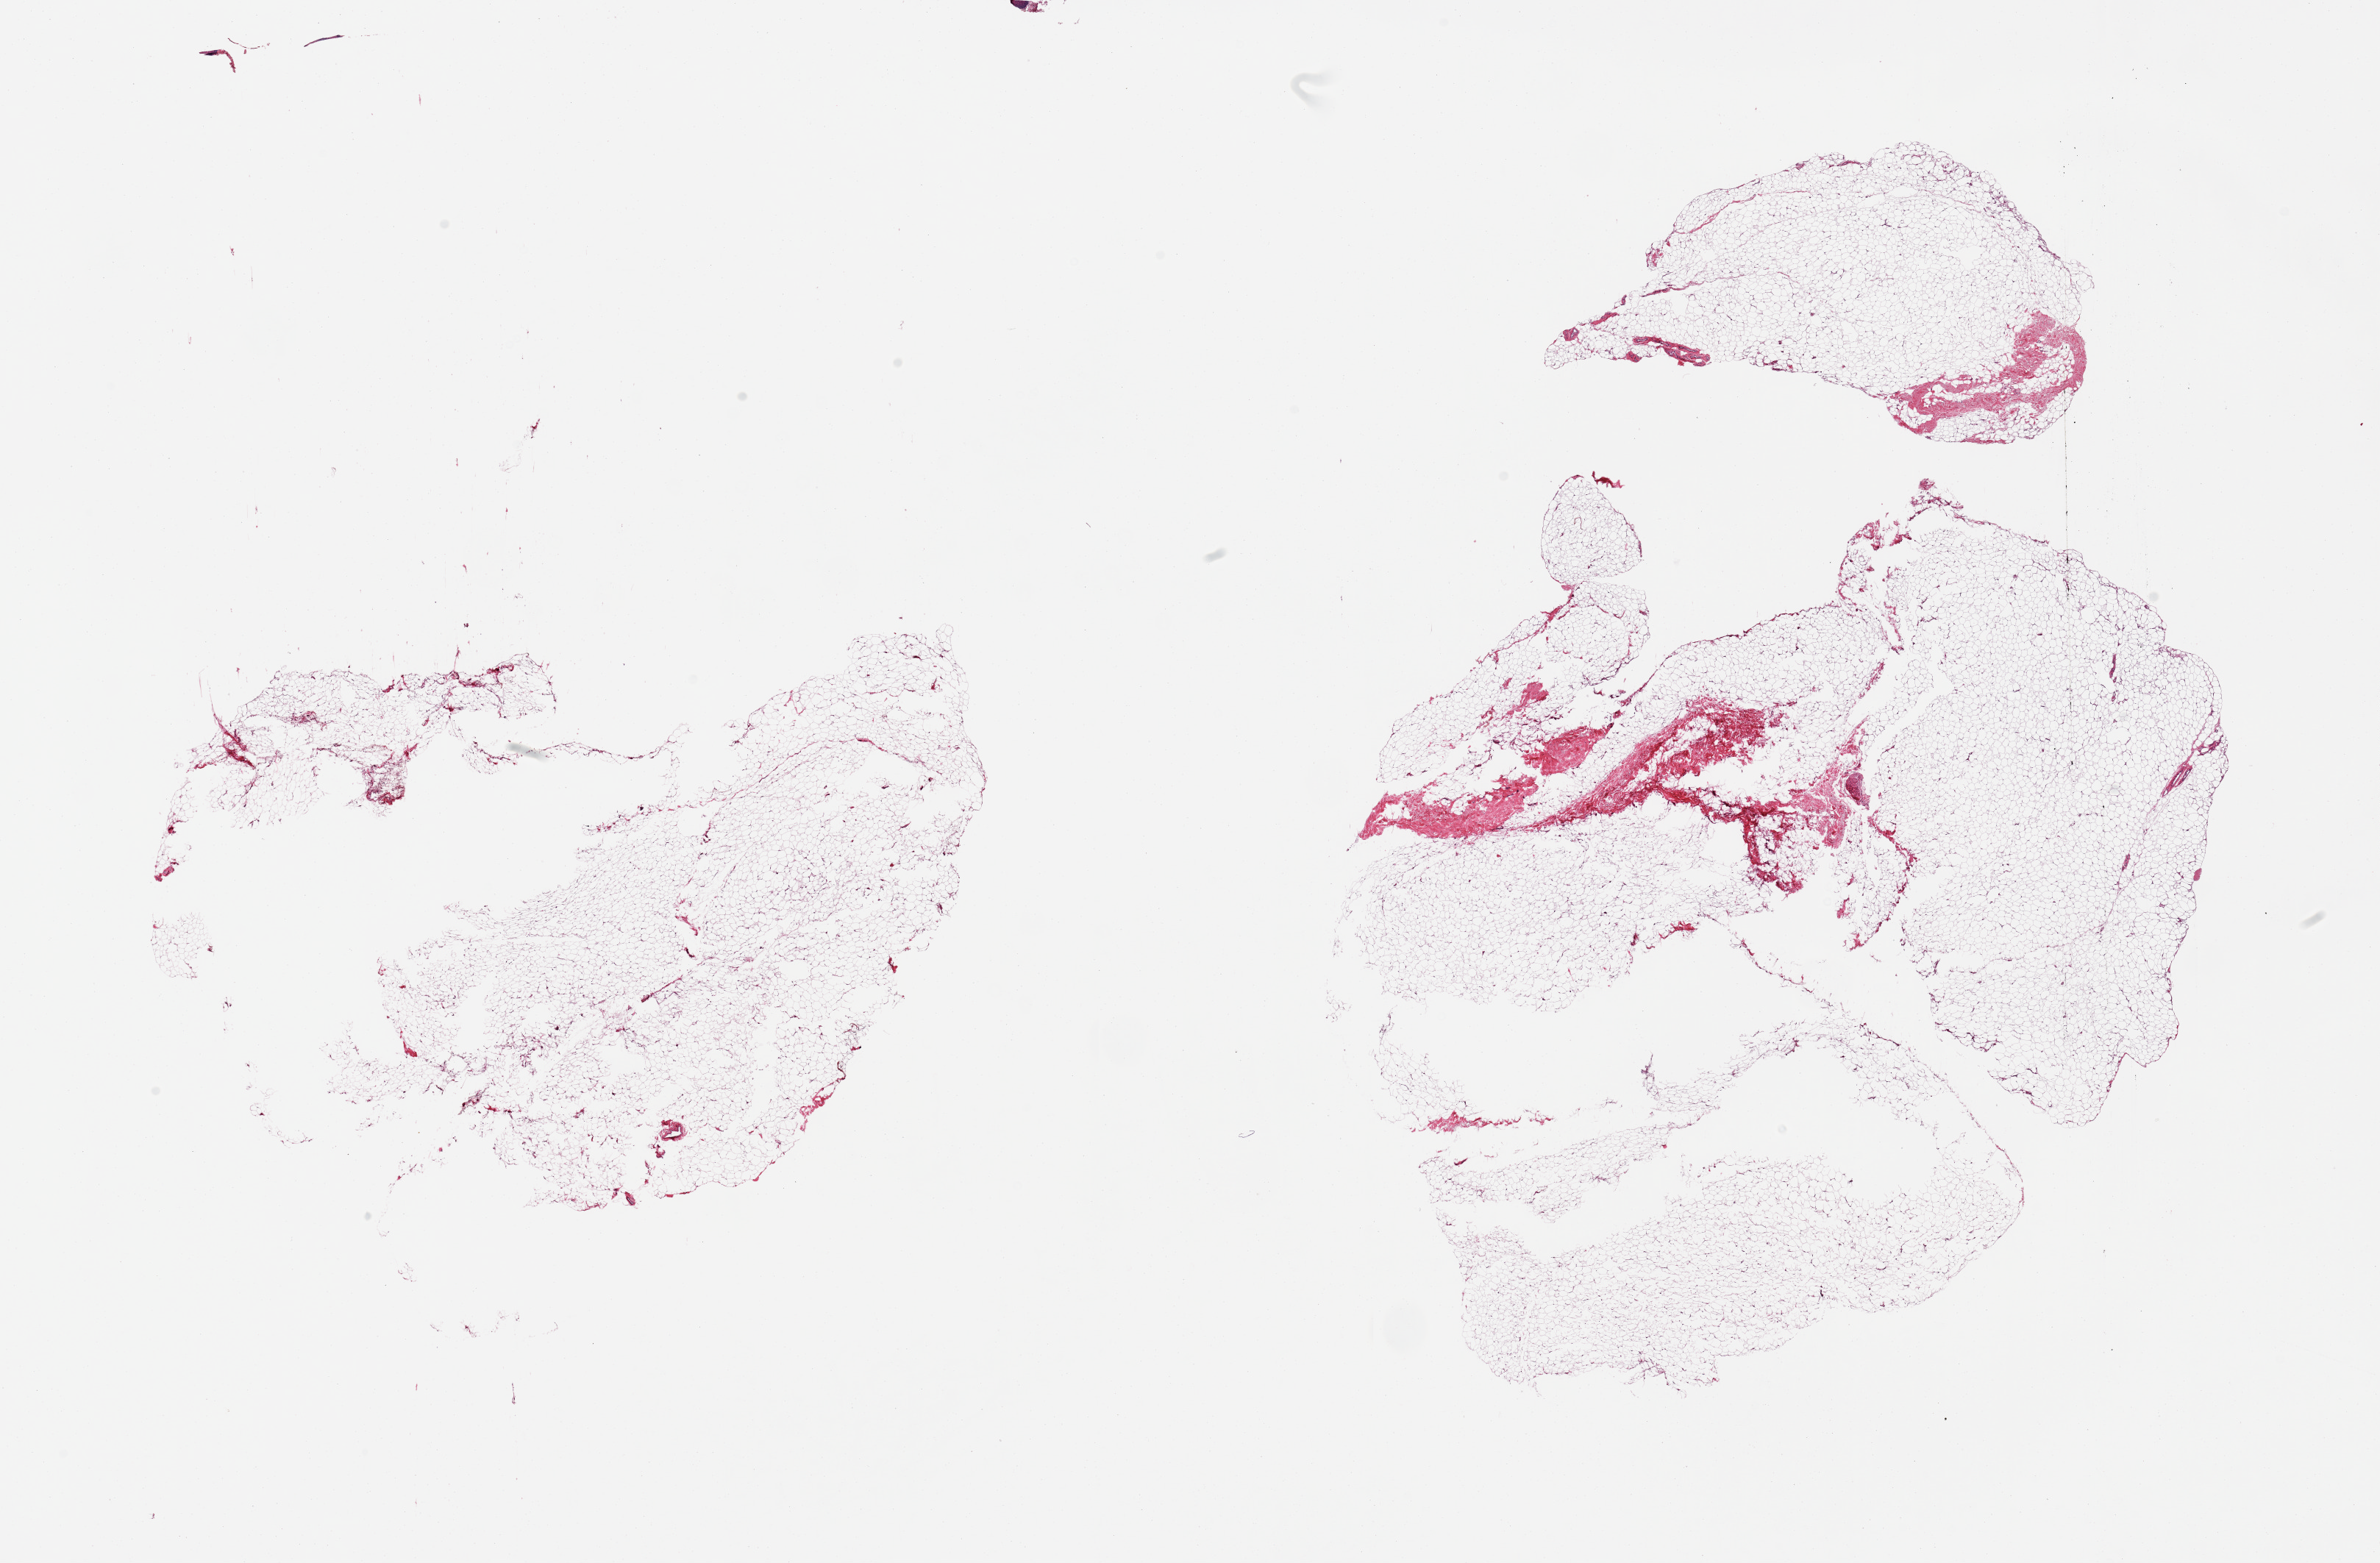
Digitized H&E-stained section — a low-resolution overview of the entire scanned area, about 25.6 x 16.8 mm, PAXgene-fixed paraffin-embedded (PFPE) section, target tissue: adipose tissue, donor tissue sample. Donor sex: female.
* reviewer comment on this tissue sample: 2 pieces; central defects (?poor fixation), minimal fibrous tissue and small nerve